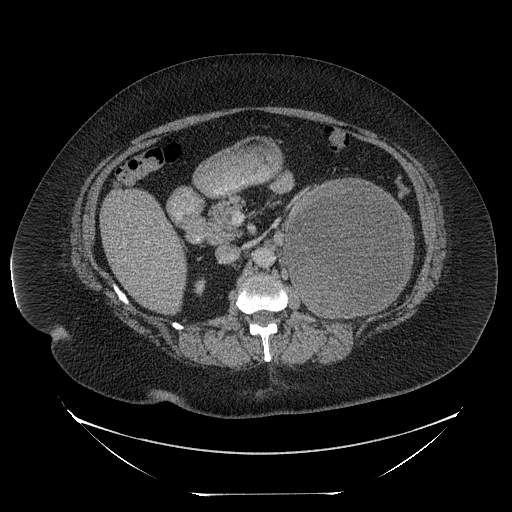
Contrast-enhanced abdominal CT, one axial slice; slice 132 of 205 in the series (ordered by position); 120 kVp; intravenous contrast given; soft-tissue window (W 400 / L 40 HU); 2.5 mm slice thickness; 512 × 512 image matrix. Female patient, age 53 years. From the clinical record (not read from this slice): diagnosis: adrenocortical carcinoma; tumour side: left adrenal; tumour size at pathology: 17 cm; Ki-67 index: 20 %; stage (as recorded): 3.
Structures marked on this image (semi-automatic segmentation, software-assisted and operator-edited):
- mass: box from (x=286, y=180) to (x=412, y=318) px